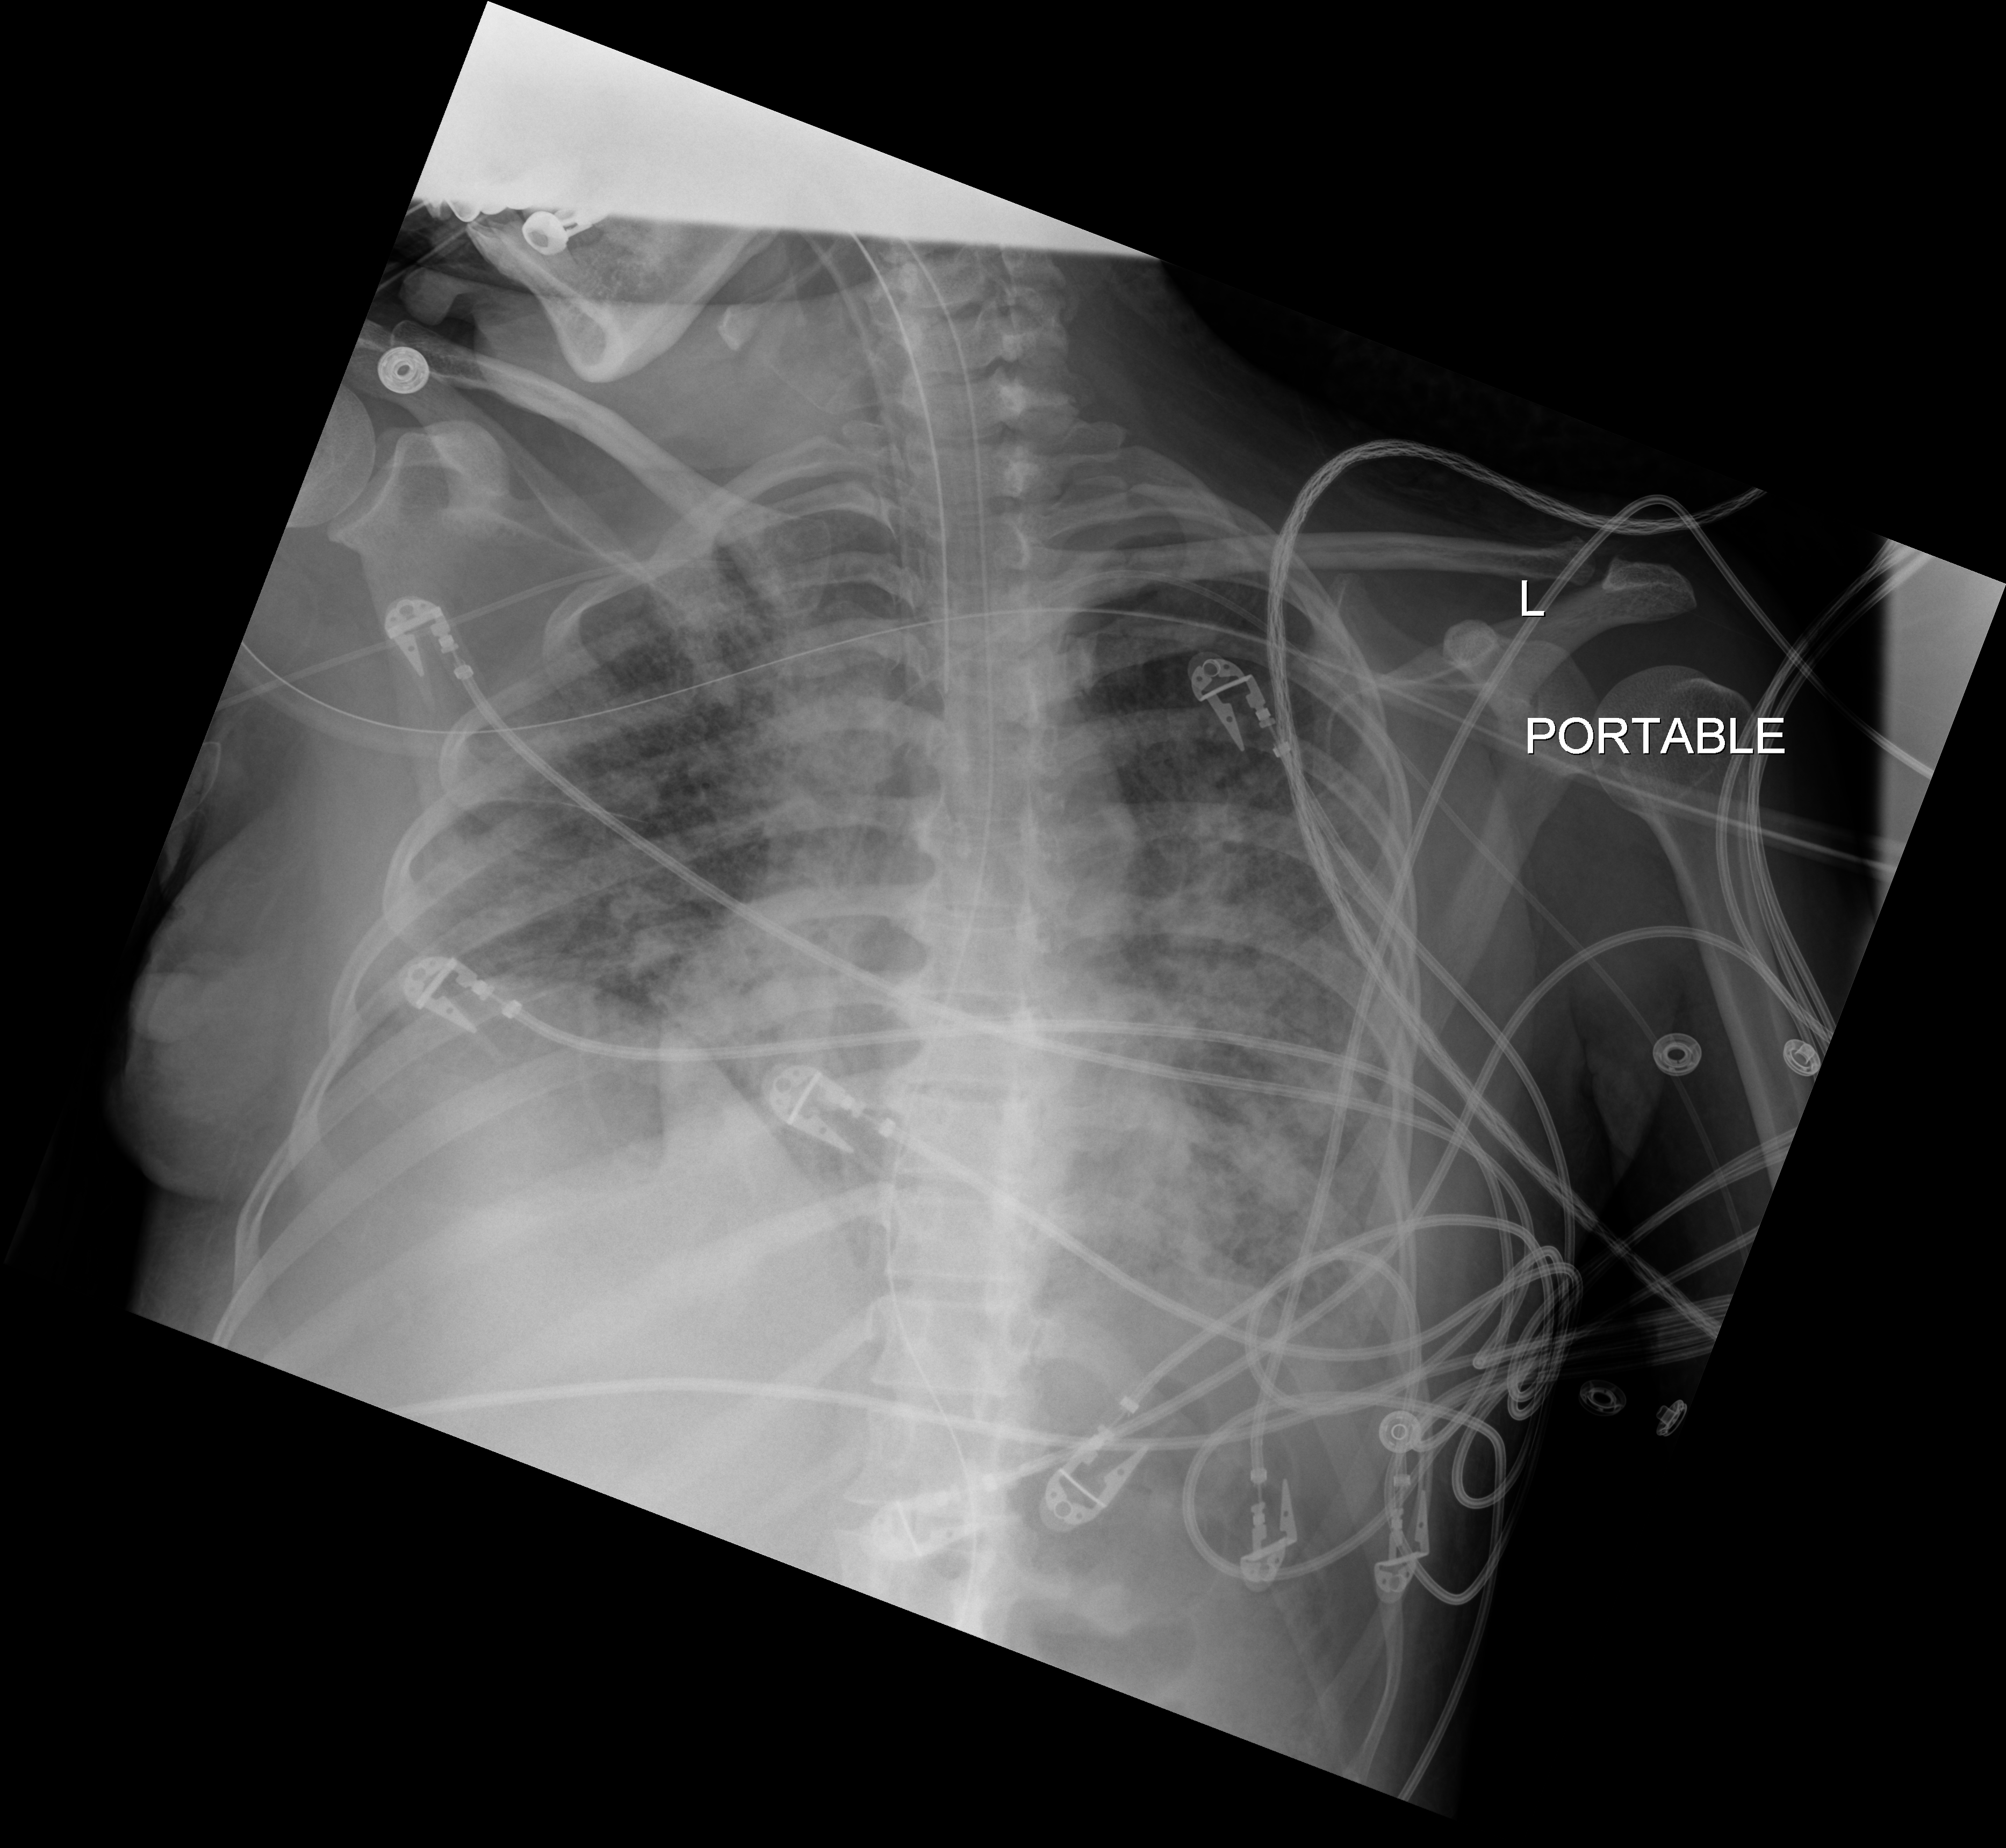
Portable chest radiograph, anteroposterior (AP) projection. Patient hospitalised with COVID-19; female, aged 18–59 years.
From the hospital-stay record, not from the radiograph (when in the stay this image was taken is not recorded):
- chronic kidney disease (admission record): no
- smoking status (admission record): former
- admitted to intensive care during this hospital stay: yes